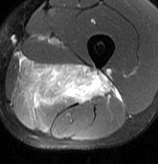
MRI of an extremity soft-tissue mass, one axial slice. Slice 38 of 70 in the series (ordered by position). T2-weighted fat-saturated. MR volume resampled by the dataset authors to the PET/CT grid (not the native acquisition matrix). 3.27 mm slice thickness. 158 × 164 image matrix, field of view 154 × 160 mm. Male patient. Case-level facts recorded for this patient, not image findings: histological type: extraskeletal osteosarcoma; grade: high; site of the primary tumour: left adductur.
Annotated regions visible in this slice (expert contour drawn on MRI and transferred to this co-registered scan by the dataset authors):
- gross tumour volume (mass): bounding box (x1, y1, x2, y2) in pixels: (15, 57, 121, 109)